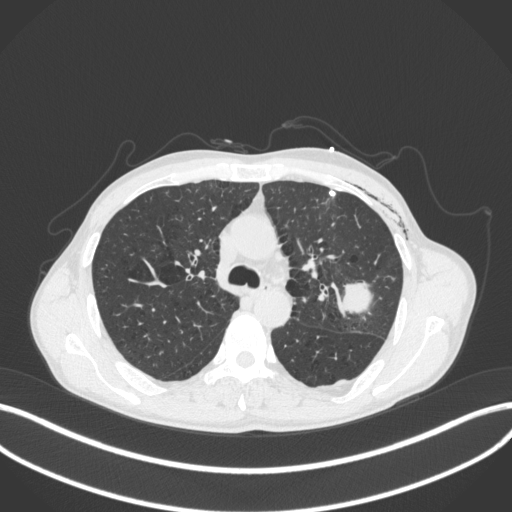
Chest CT, one axial slice. Slice 269 of 416 in the series (ordered by position). Reconstruction kernel B31f. 120 kVp. Lung window (W 1500 / L -600 HU). 1 mm slice thickness. 512 × 512 image matrix, field of view 400 × 400 mm. Male patient, age 58 years. From the clinical record (not read from this slice): clinical TNM (as recorded): T3 N0 M0.
Annotated regions visible in this slice (rectangle marked by the reading radiologist):
- lung tumour (recorded histology: adenocarcinoma): bounding box (x1, y1, x2, y2) in pixels: (329, 271, 373, 322)